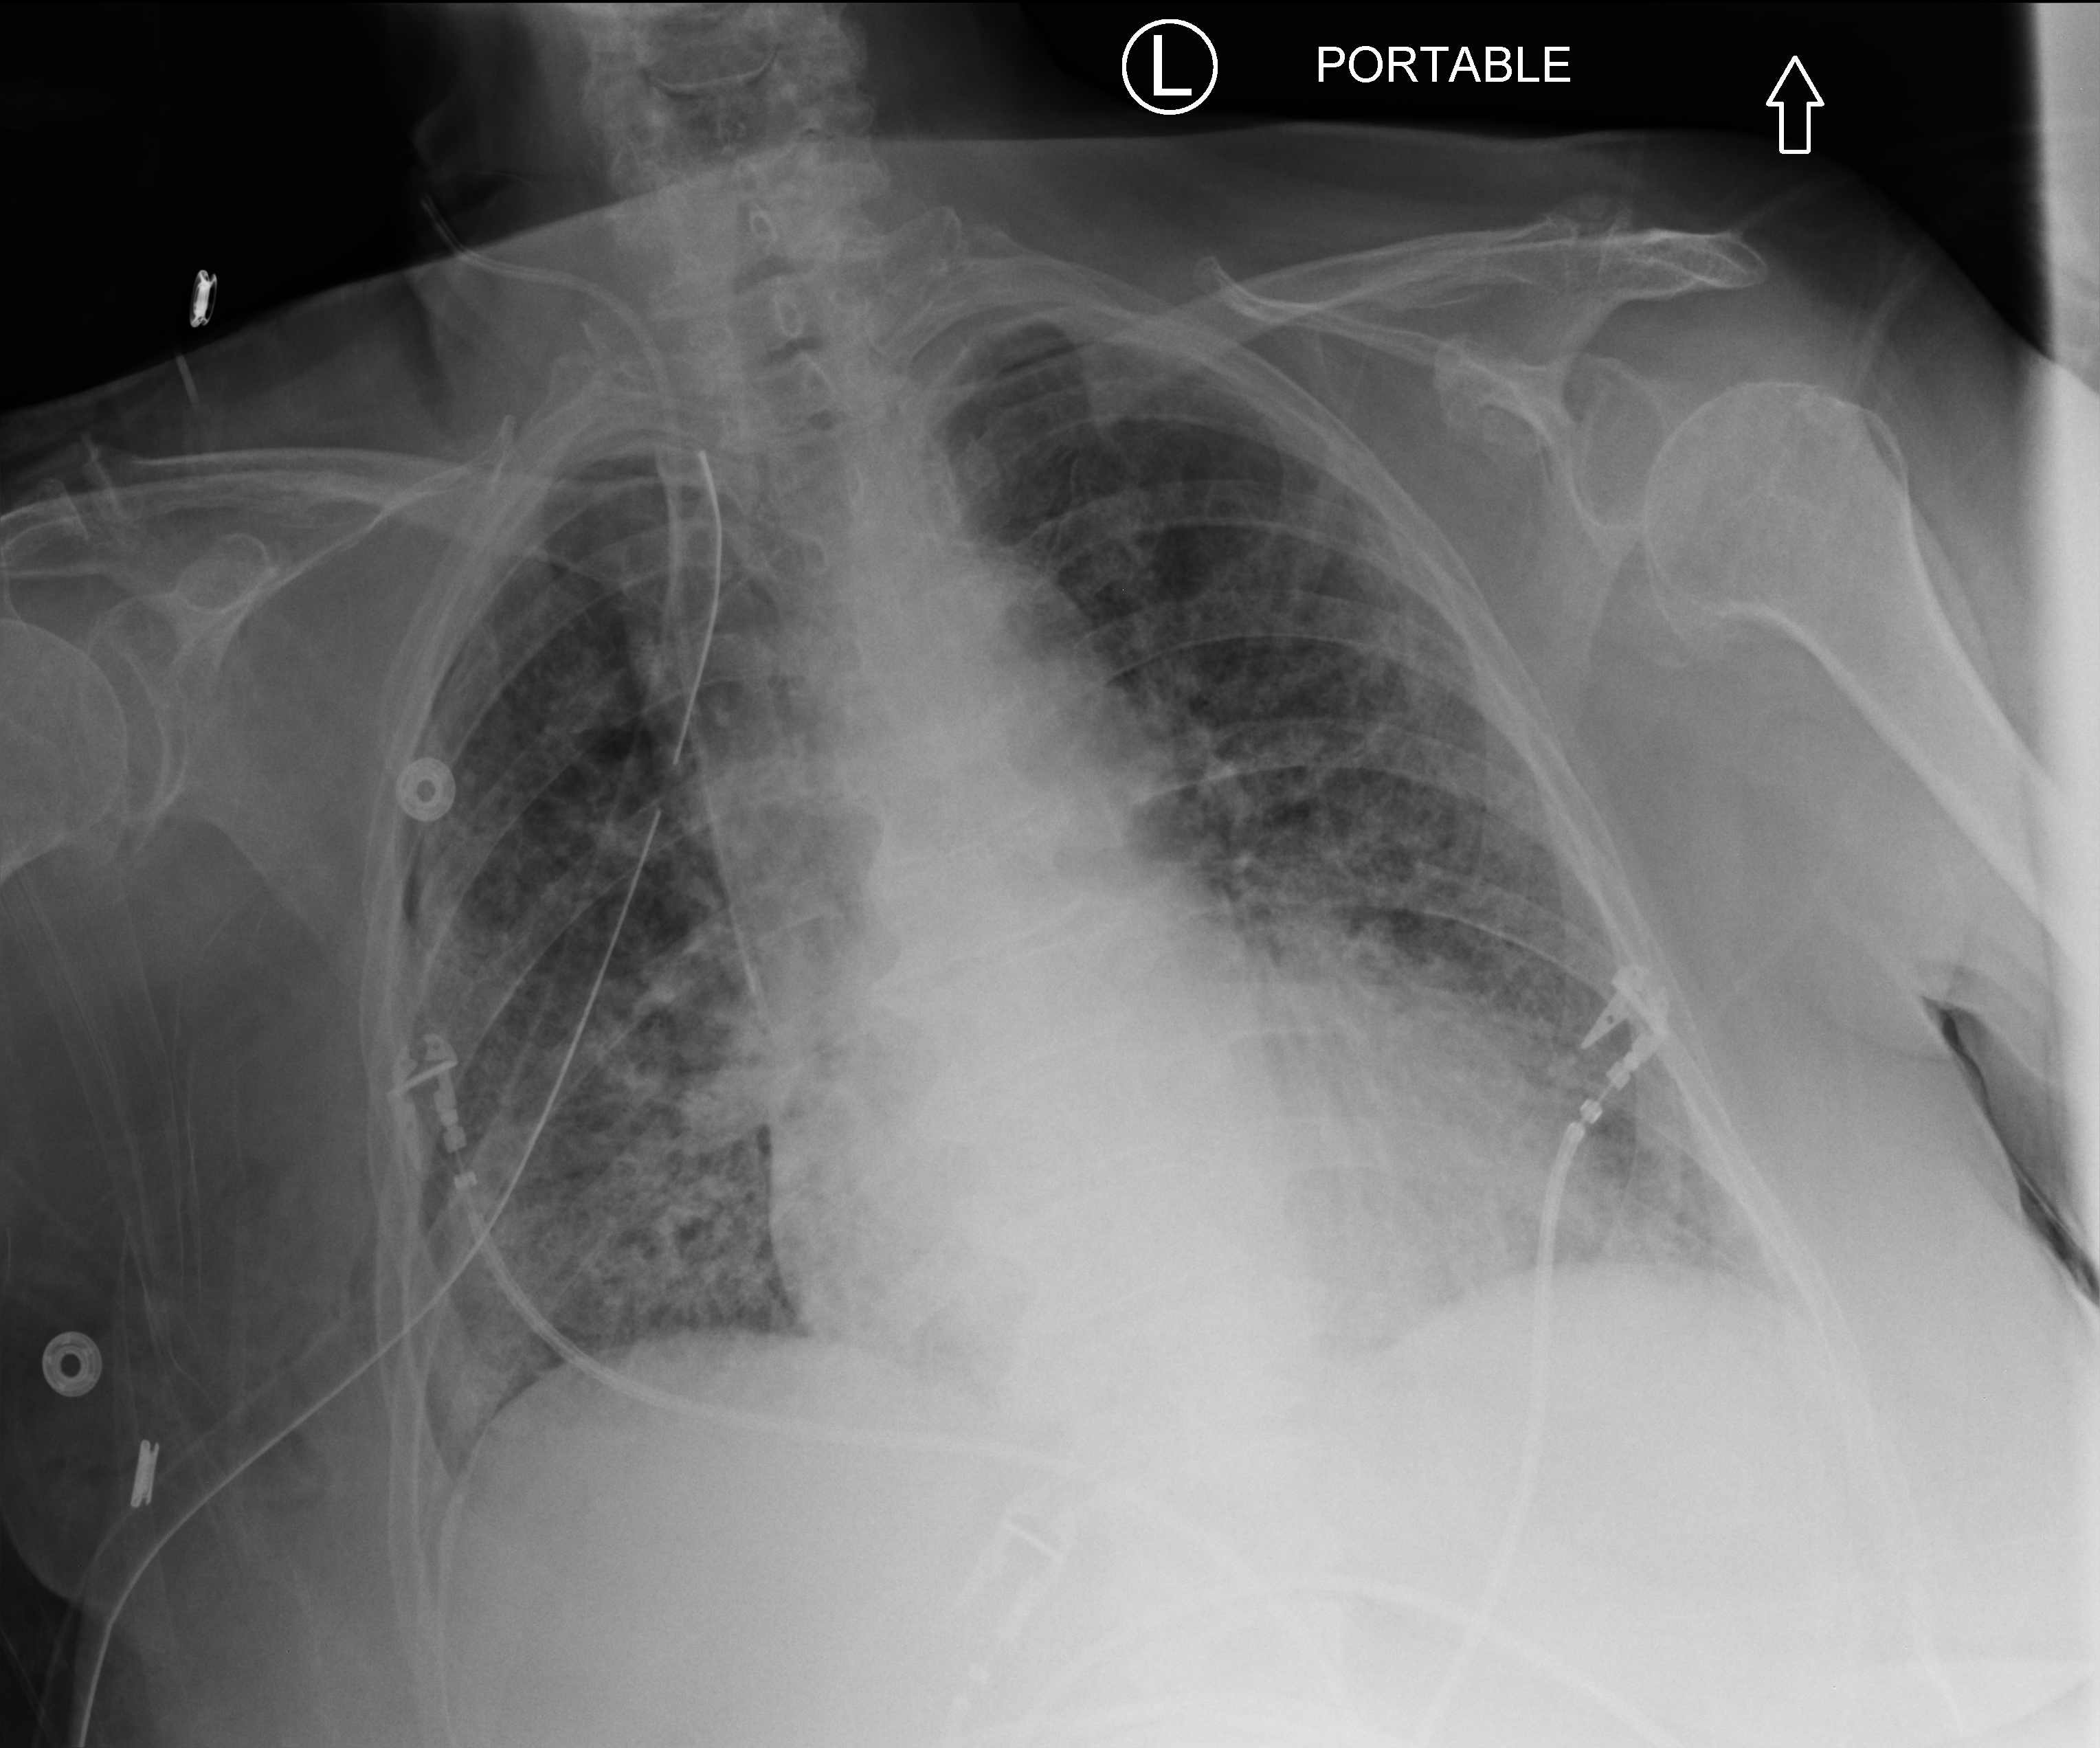
Portable chest radiograph, anteroposterior (AP) projection. Female patient hospitalised with COVID-19, age 75–90 years.
Admission-level facts for this patient (not findings on this image; timing relative to this image not recorded):
- hypertension (admission record): no
- mechanically ventilated during this hospital stay: yes
- admitted to intensive care during this hospital stay: no